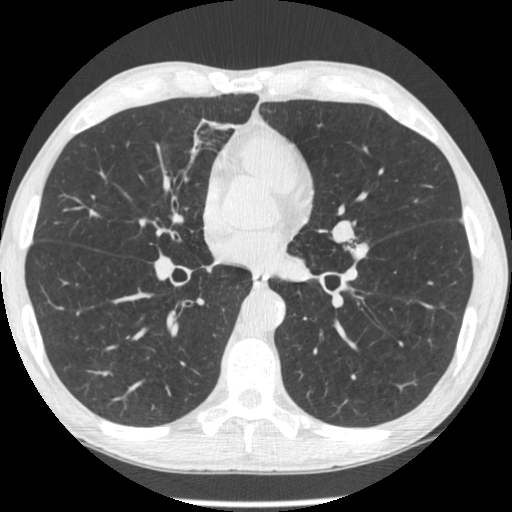
Low-dose screening chest CT, one axial slice. Reconstruction kernel STANDARD. 120 kVp. Lung window (W 1500 / L -600 HU). 1.25 mm slice thickness. 512 × 512 image matrix, field of view 326 × 326 mm.
Annotated regions visible in this slice (manually delineated by an expert):
- lesion 1 (tumor, upper lobe of left lung): bounding box <351,244,368,258> (left, top, right, bottom; pixels)